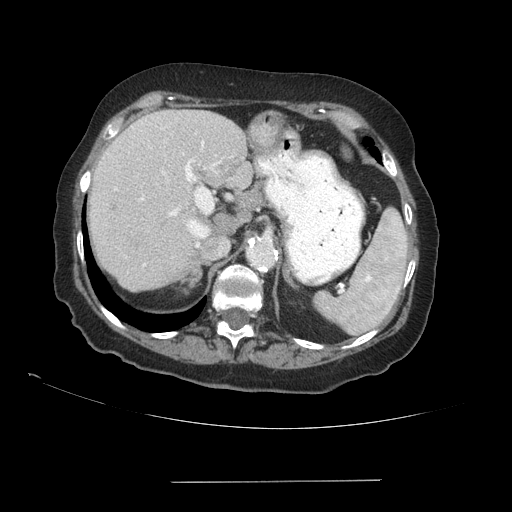
Contrast-enhanced abdominal CT (liver protocol), one axial slice; 140 kVp; soft-tissue window (W 400 / L 40 HU); 2.5 mm slice thickness; 512 × 512 image matrix, field of view 400 × 400 mm. Case-level facts recorded for this patient, not image findings: diagnosis: hepatocellular carcinoma (patient treated with transarterial chemoembolisation; whether this scan precedes or follows treatment is not stated here); TNM stage (as recorded): Stage-IVA; Child-Pugh class: A; tumour nodularity: uninodular.
Outlined on this slice (semi-automatically segmented with operator editing):
- liver parenchyma outside the tumour (the mass and vessels are separate outlines, so this box may not span the whole liver): bounding box [x1, y1, x2, y2] px = [88, 110, 252, 290]
- liver vessels: [115, 141, 220, 266]